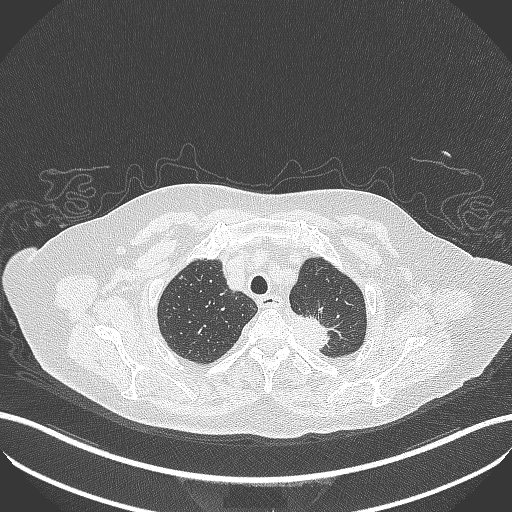
Chest CT, one axial slice; slice 292 of 353 in the series (ordered by position); lung window (W 1500 / L -600 HU); 1 mm slice thickness; 512 × 512 image matrix, field of view 400 × 400 mm. Female patient, age 81 years. From the clinical record (not read from this slice): clinical TNM (as recorded): T2a N0 M0.
Outlined on this slice (bounding box drawn by a radiologist):
- lung tumour (recorded histology: adenocarcinoma): bounding box <287,306,345,356> (left, top, right, bottom; pixels)